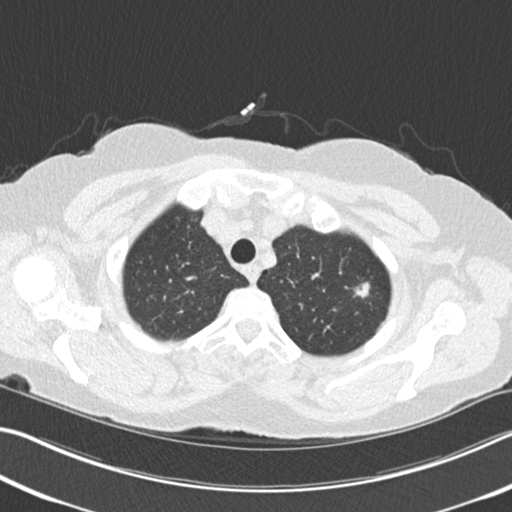
Low-dose screening chest CT, one axial slice. Reconstruction kernel B30f. Lung window (W 1500 / L -600 HU). 512 × 512 image matrix, field of view 342 × 342 mm.
Structures marked on this image (outlined manually by an expert reader):
- lesion 1 (tumor): bounding box <354,282,370,298> (left, top, right, bottom; pixels)